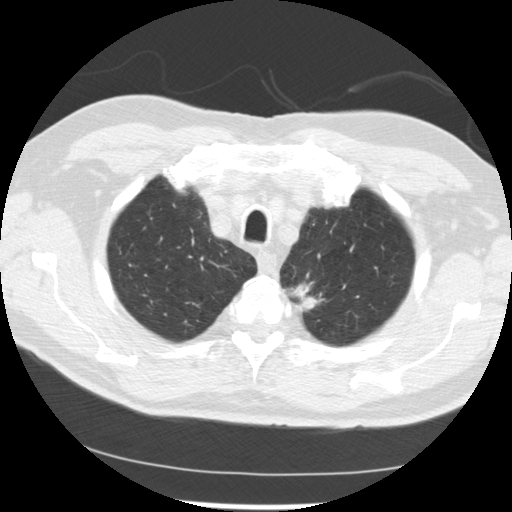
Low-dose screening chest CT, axial slice. Baseline screening round. Lung window (W 1500 / L -600 HU). Slice 210 of 249 in the series. Male, age 71 years at enrolment. Current smoker at enrolment.
Lesion marked by an expert reader, bounding box [x1, y1, x2, y2] px = [270, 271, 337, 321]. The screening reader recorded 2 non-calcified nodules or masses ≥4 mm on this exam; which of them this box marks is not recorded. Official screen result: positive, change unspecified: nodule(s) >= 4 mm or enlarging nodule(s), mass(es), or other non-specific abnormalities suspicious for lung cancer.